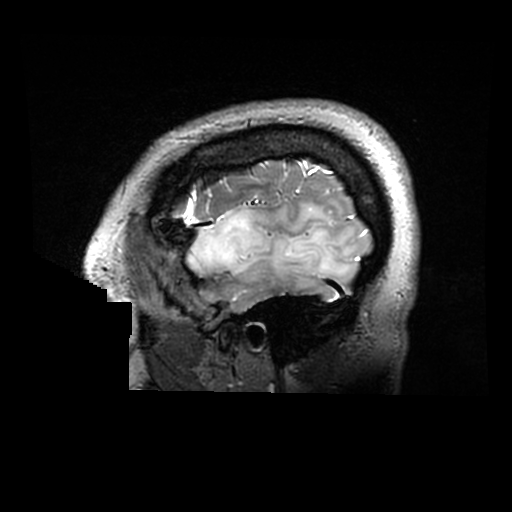
Brain MRI from a brain-tumour surgery series, one sagittal slice. Slice 247 of 320 in the series (ordered by position). 0.6 mm slice thickness. 512 × 512 image matrix, field of view 240 × 240 mm. Case-level facts recorded for this patient, not image findings: histopathology: Astrocytoma; WHO grade: 2; IDH mutation: yes.
Annotated regions visible in this slice (manually delineated by an expert):
- tumour: bounding box (x1, y1, x2, y2) in pixels: (188, 202, 353, 287)